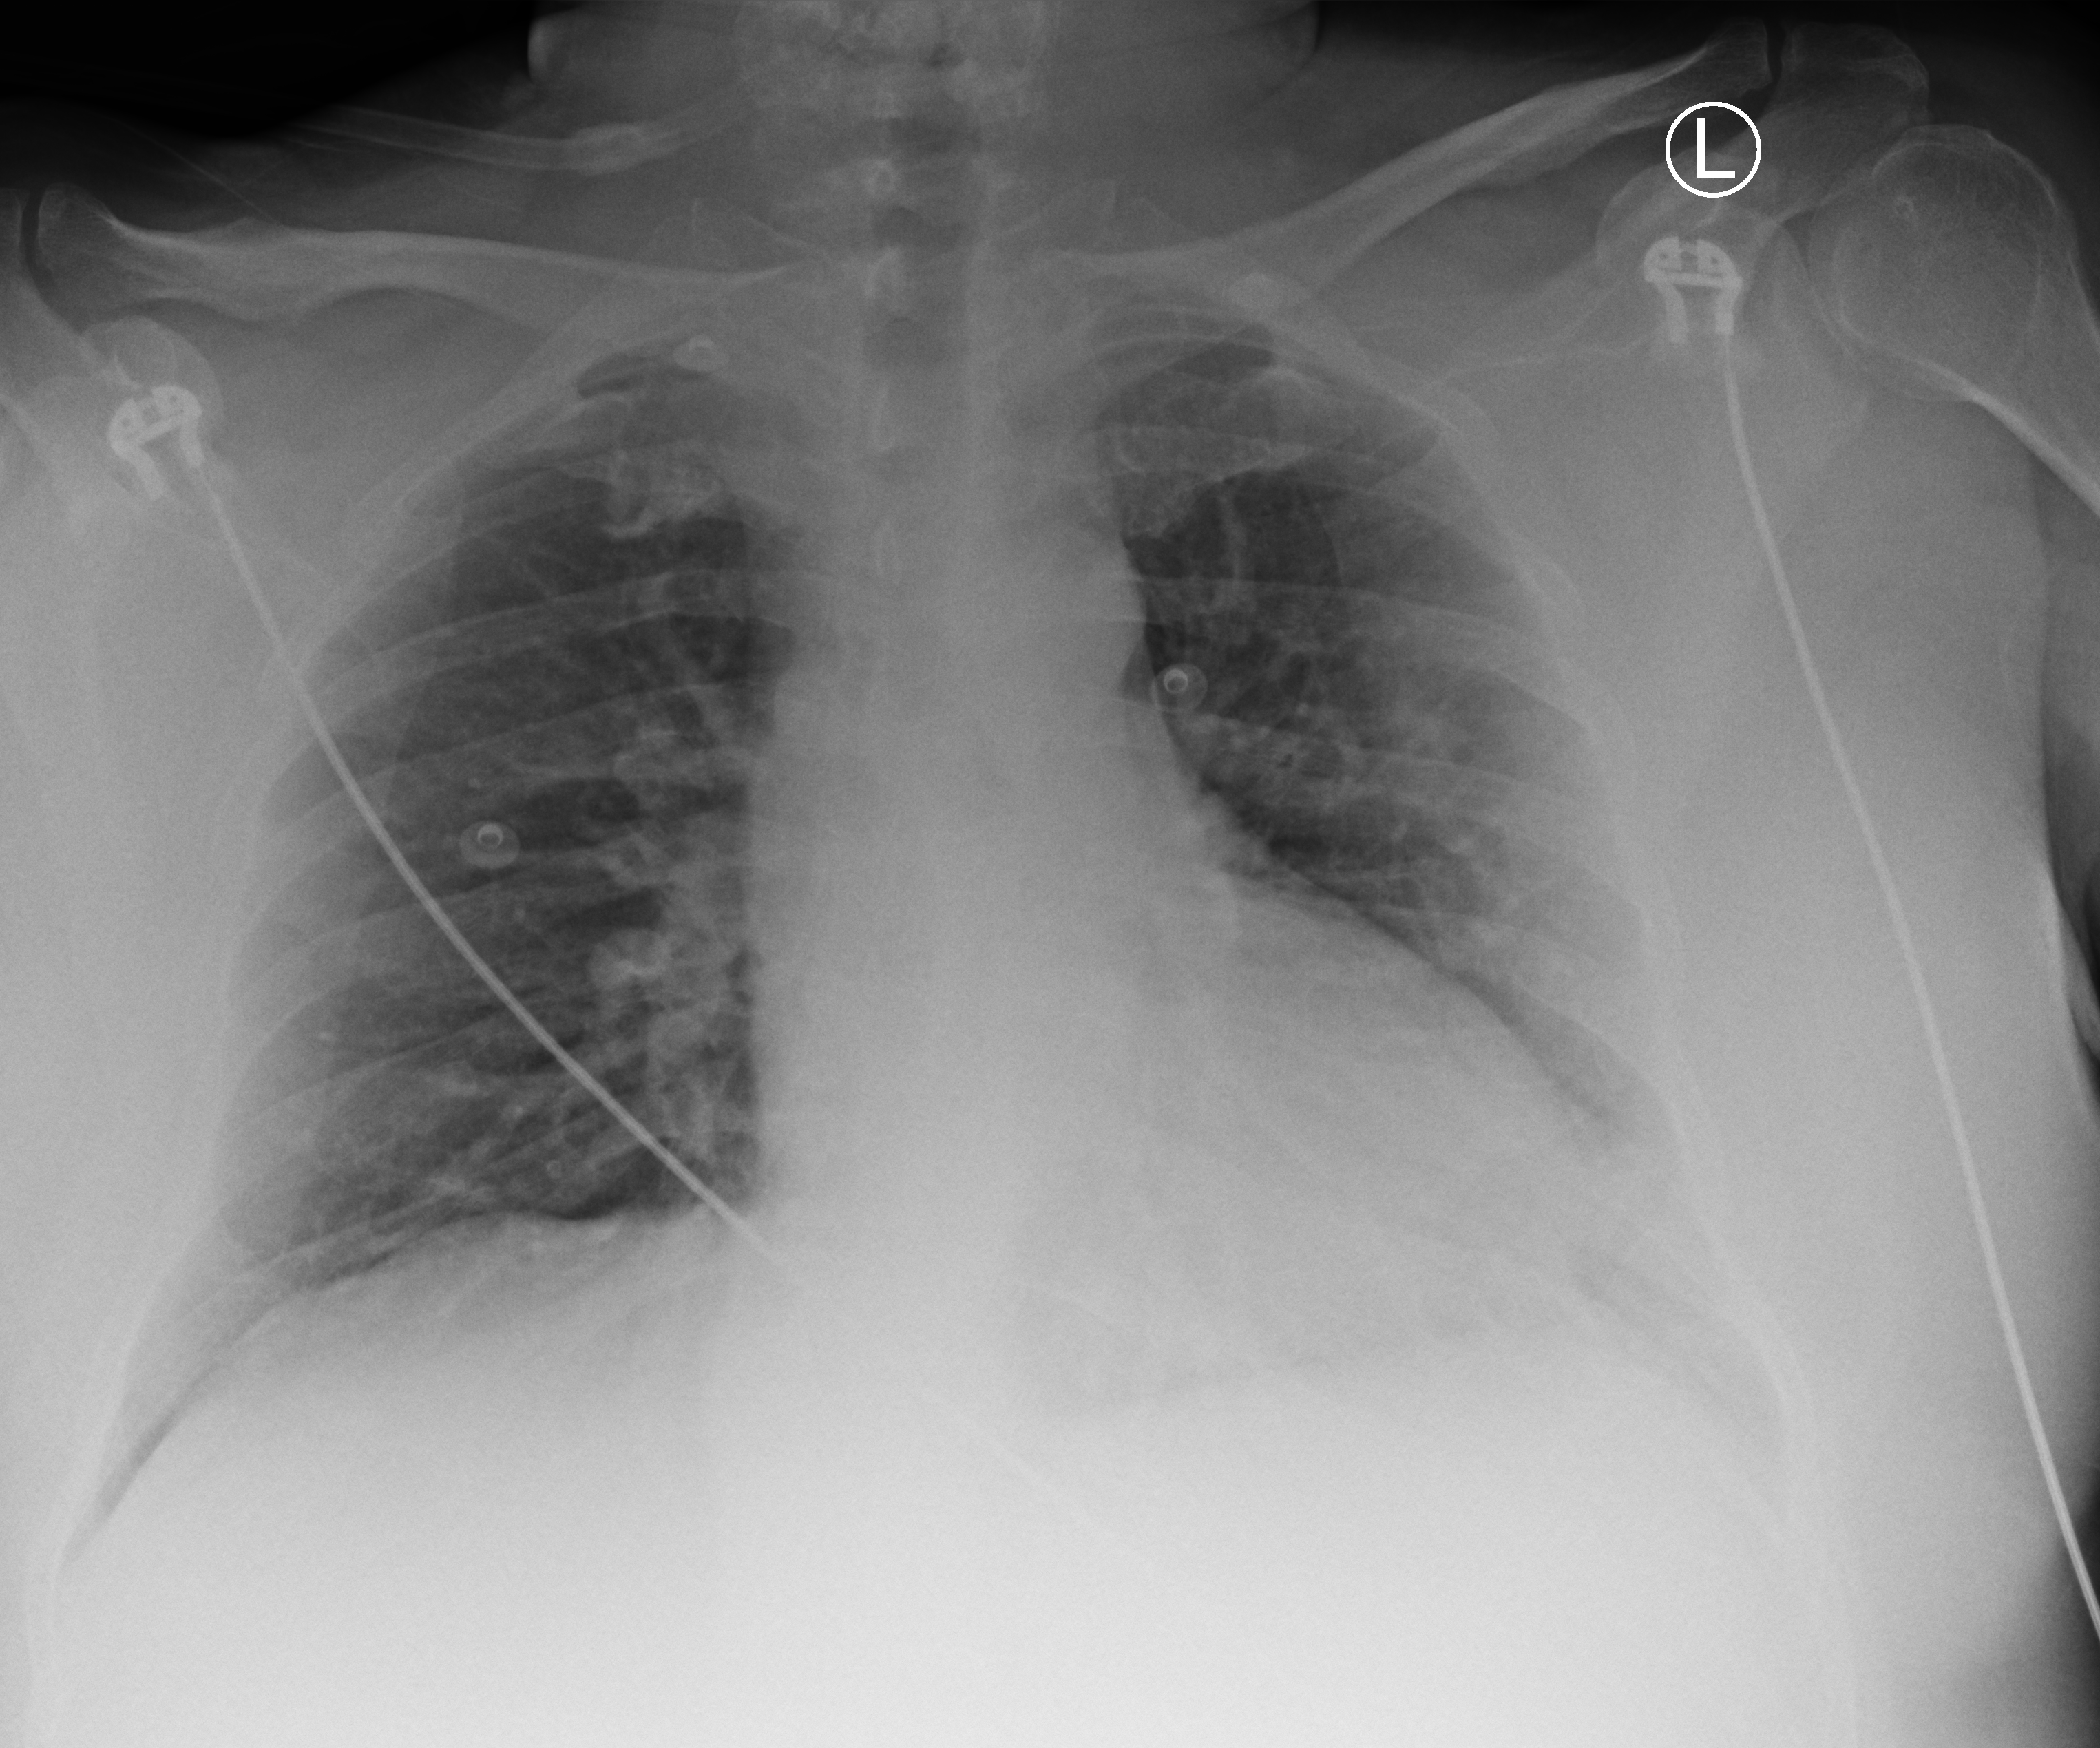
Chest X-ray (portable). Patient hospitalised with COVID-19; male, aged 18–59 years.
Hospital-stay facts (about this admission, not read from this image; timing relative to this image not recorded):
- hypertension (admission record): yes